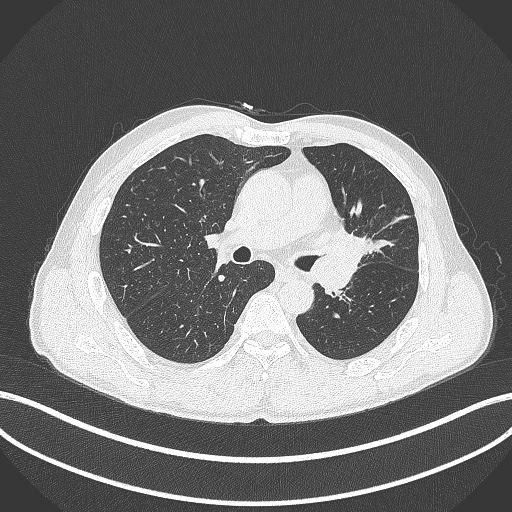
Chest CT, one axial slice. Slice 248 of 429 in the series (ordered by position). Reconstruction kernel B70f. 120 kVp. Lung window (W 1500 / L -600 HU). 1 mm slice thickness. 512 × 512 image matrix. Male patient, age 57 years. Case-level facts recorded for this patient, not image findings: clinical TNM (as recorded): T2b N0 M0.
Annotated regions visible in this slice (bounding box drawn by a radiologist):
- lung tumour (recorded histology: squamous cell carcinoma): bounding box [x1, y1, x2, y2] px = [321, 221, 372, 259]